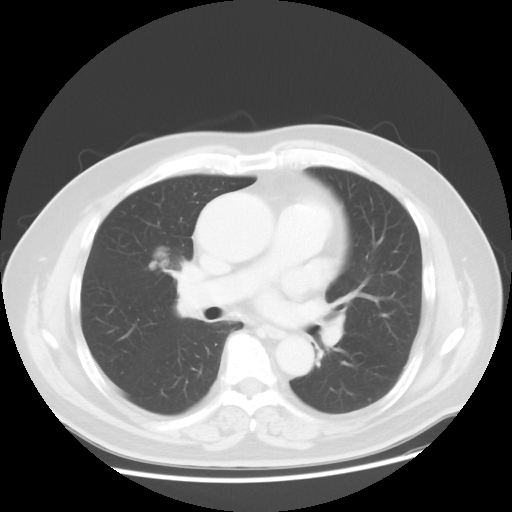
Chest CT, one axial slice; position 23 of 48 along the scan axis; 120 kVp; lung window (W 1500 / L -600 HU); 5 mm slice thickness; 512 × 512 image matrix, field of view 392 × 392 mm. Male patient, age 60 years. From the clinical record (not read from this slice): clinical TNM (as recorded): T2 N3 M0; histopathological grade: G2-3.
Annotated regions visible in this slice (rectangle marked by the reading radiologist):
- lung tumour (recorded histology: adenocarcinoma): bounding box (x1, y1, x2, y2) in pixels: (142, 226, 196, 285)